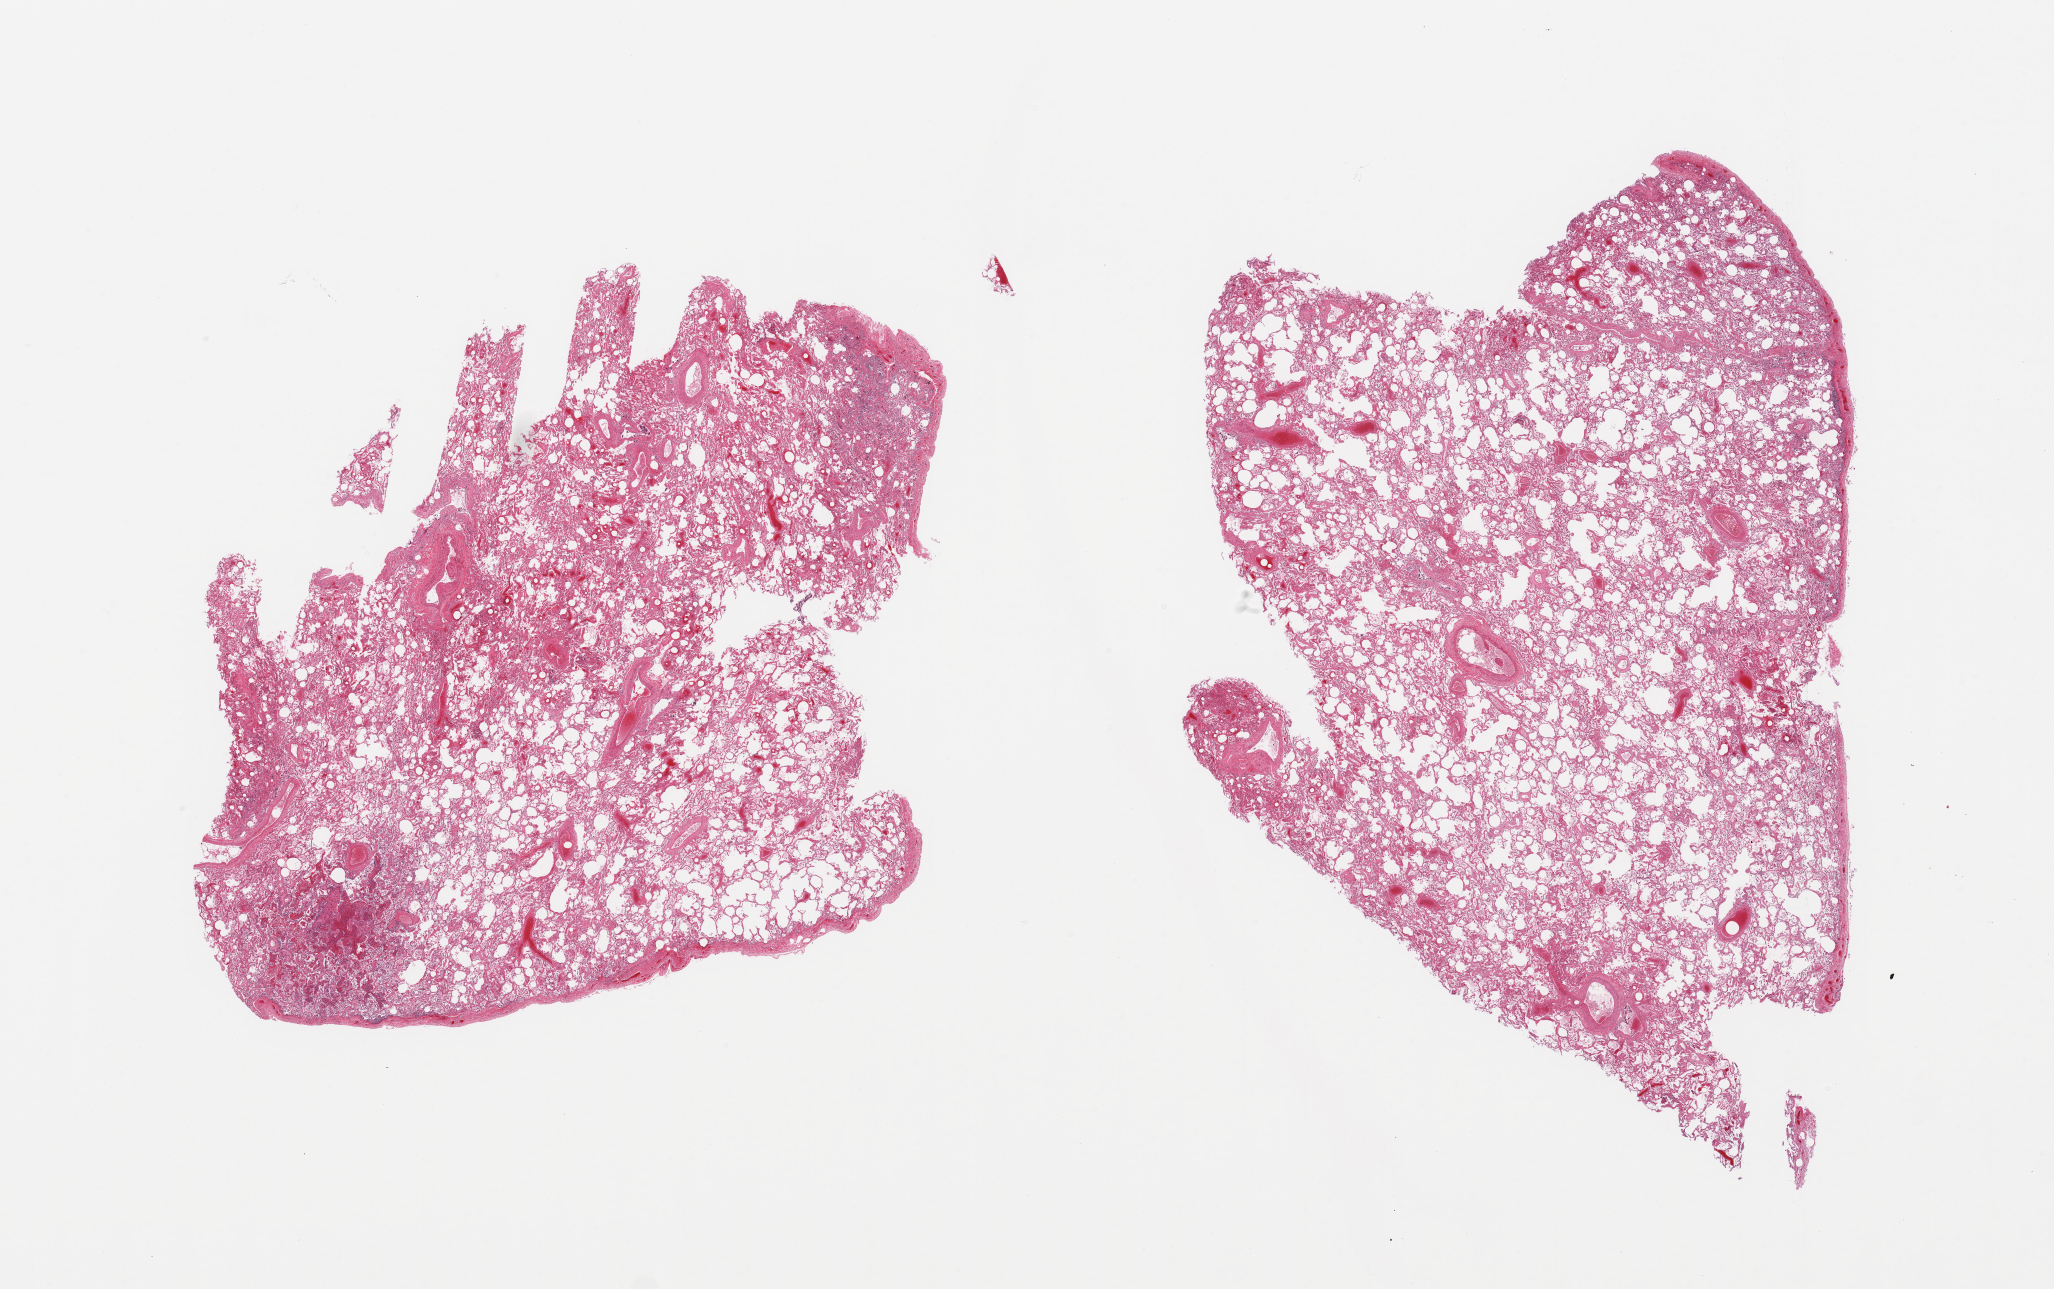
Digitized hematoxylin and eosin (H&E)-stained section, brightfield, a low-resolution overview of the entire scanned area, about 32.5 x 20.4 mm; PAXgene-fixed, paraffin-embedded tissue; sampled site (target tissue): lung; donor tissue sample. Donor: male.
Review note (as recorded): 2 pieces; pulmonary tissue with pleura; massive congestion; patchy subpleural lymphocytic infiltrates; focal inflammatory cell infiltrate with fresh hemorrhage; thick-walled vessels.